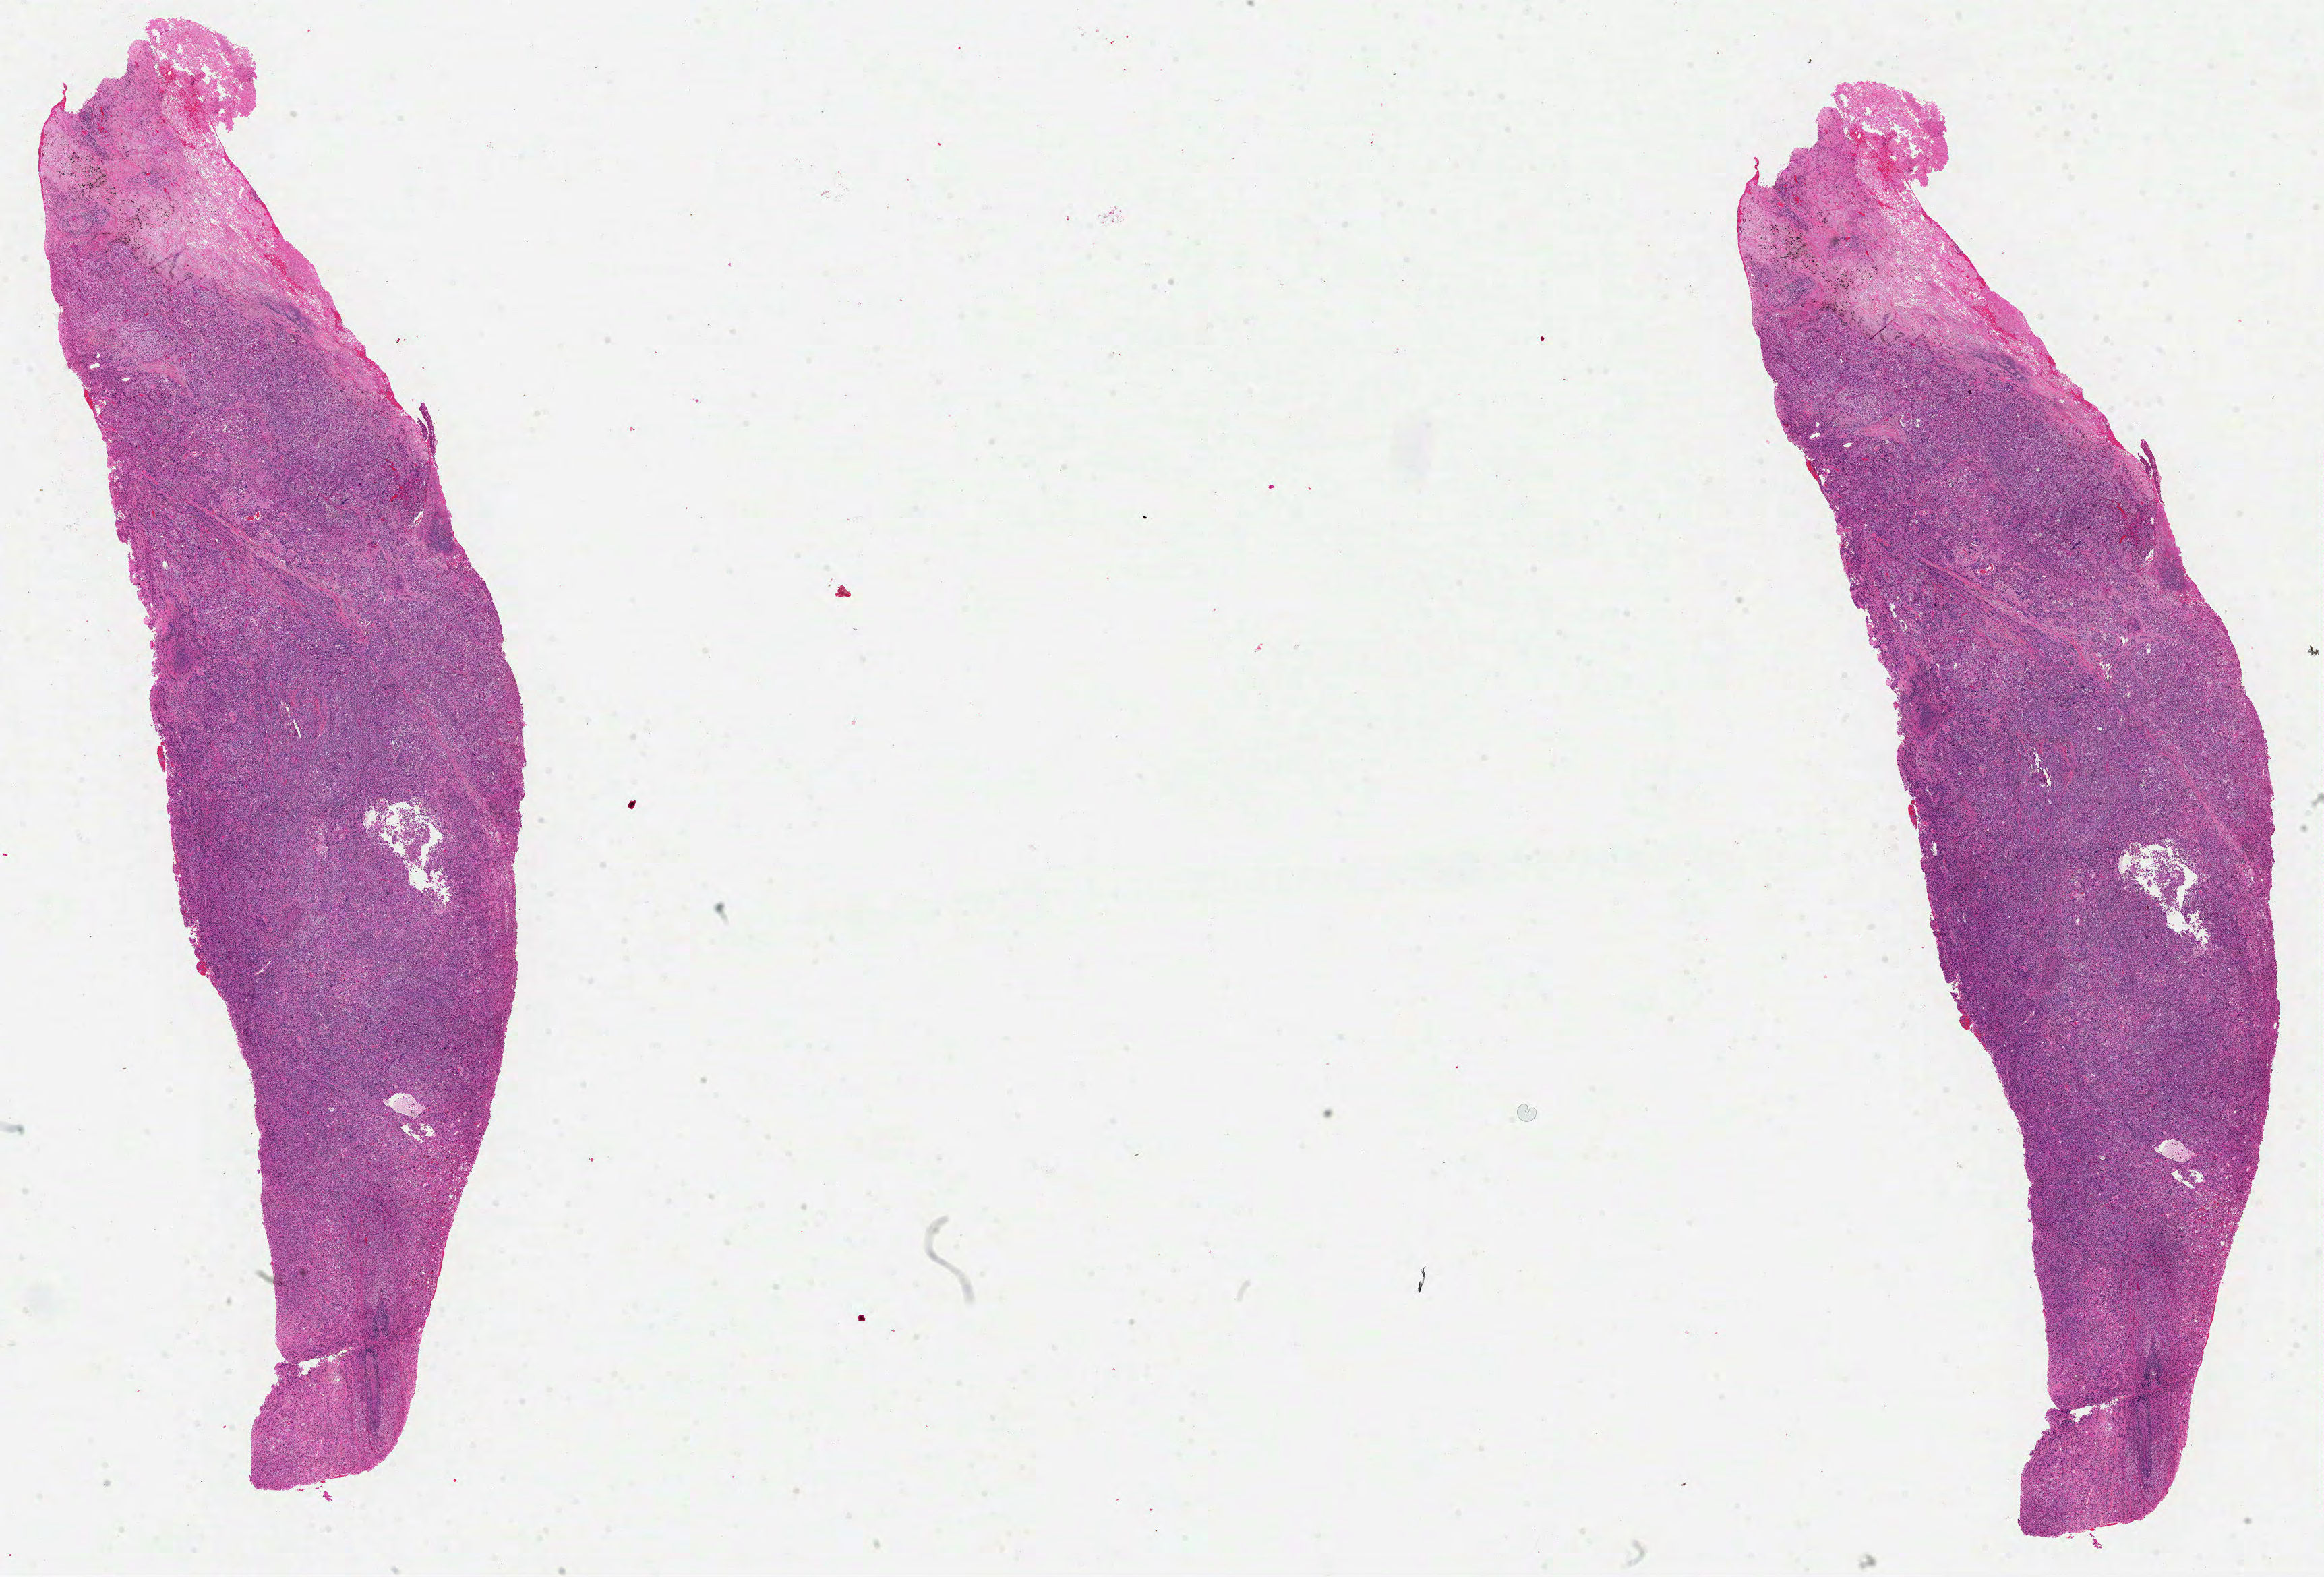
Whole-slide histology image, Hematoxylin and eosin (H&E) stained — whole scanned area (about 27.8 x 18.9 mm, slide scanned at 40x) shown as a low-resolution overview. Formalin-fixed paraffin-embedded (FFPE) diagnostic section. Sample: primary tumour, lung. Male, age 68 years at initial diagnosis.
• laterality: right
• AJCC pathologic stage: IIB
• TNM: T3 N0 M0
• diagnosis: Adenocarcinoma, NOS (upper lobe, lung)